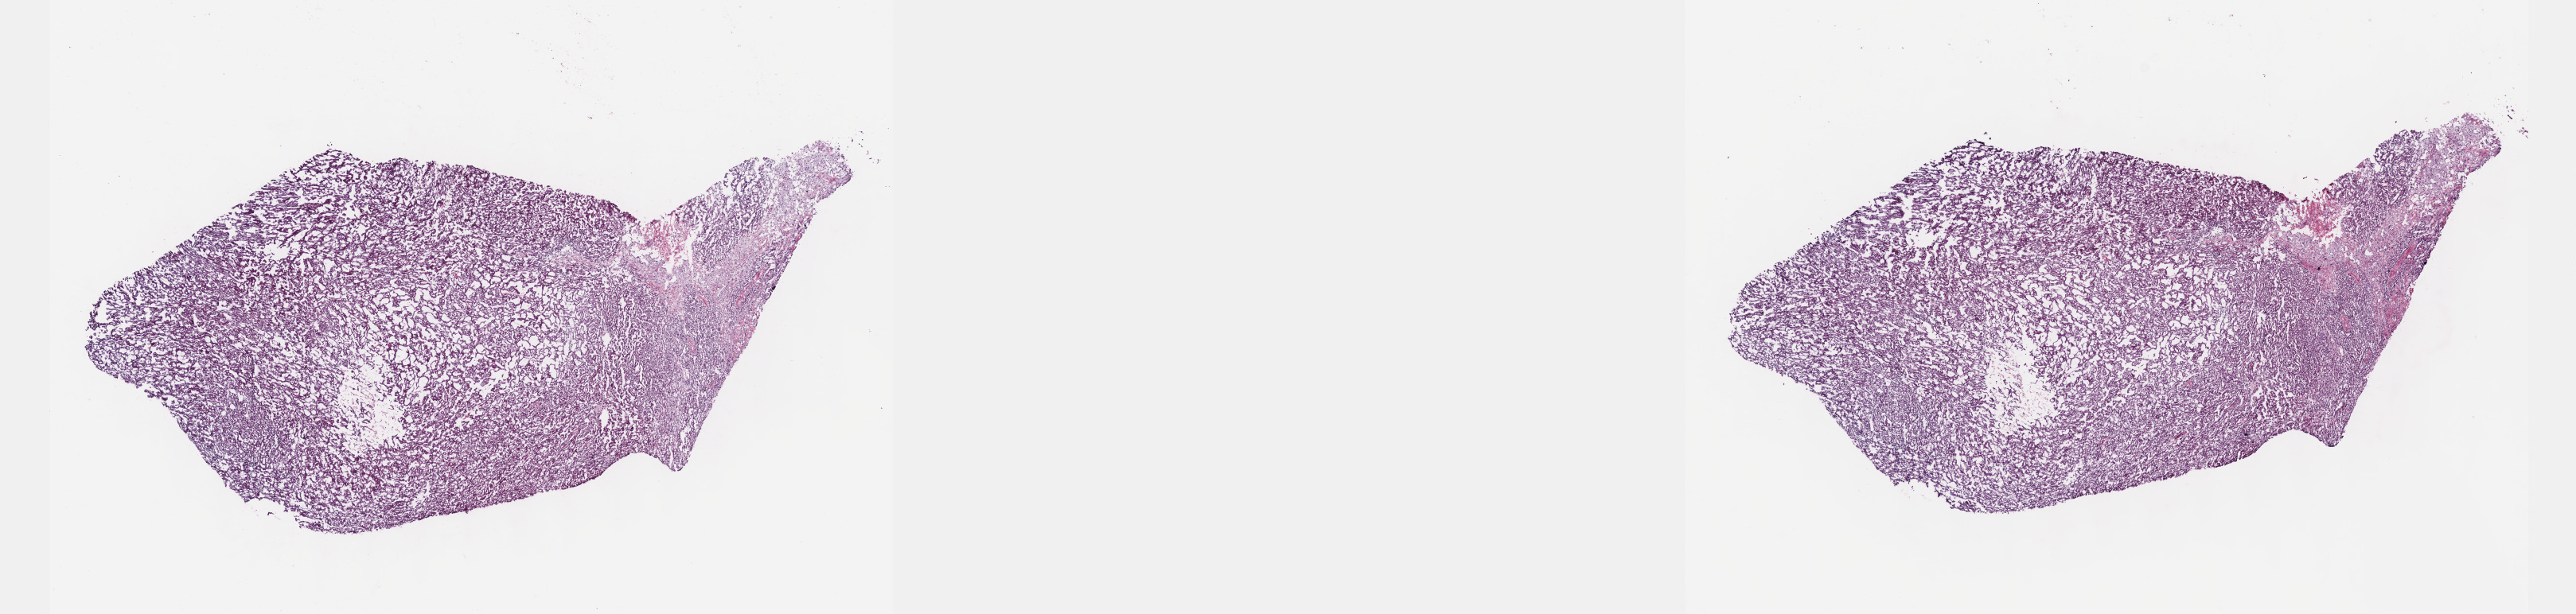
Hematoxylin and eosin (H&E) stained whole-slide image — shown as a low-resolution overview of the whole scanned area (about 26.2 x 6.2 mm); frozen section from the top of the tissue portion; kidney, primary tumour sample. Male, age 48 years at initial diagnosis. Pathologist review of this section (percent, as recorded): tumour cells 90%, tumour nuclei 95%, normal cells 0%, stromal cells 10%, necrosis 0%. Infiltration values recorded for this section: lymphocyte infiltration 0%, monocyte infiltration 0%, neutrophil infiltration 0%.
AJCC pathologic stage: I (7th edition). Pathologic diagnosis: Papillary adenocarcinoma, NOS.